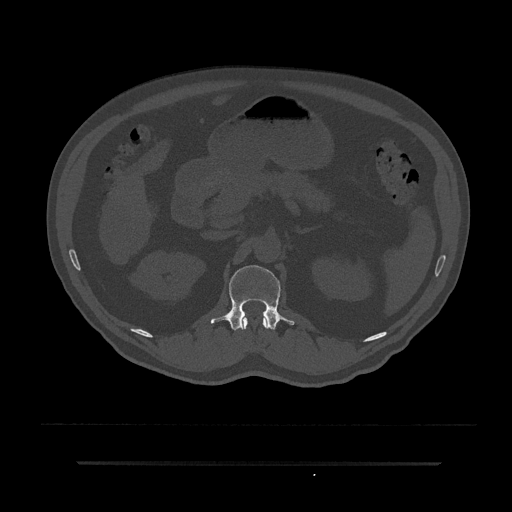
CT including the spine, one axial slice. Position 162 of 797 along the scan axis. Bone window (W 1800 / L 400 HU). 512 × 512 image matrix. Male patient, age 59 years. From the clinical record (not read from this slice): primary cancer: bile ducts; vertebrae with lytic lesions (as recorded): T10.
Annotated regions visible in this slice (semi-automatic segmentation, software-assisted and operator-edited):
- L1 vertebra: box from (x=210, y=265) to (x=294, y=331) px
- T12 vertebra: (x=241, y=315)–(x=268, y=330)